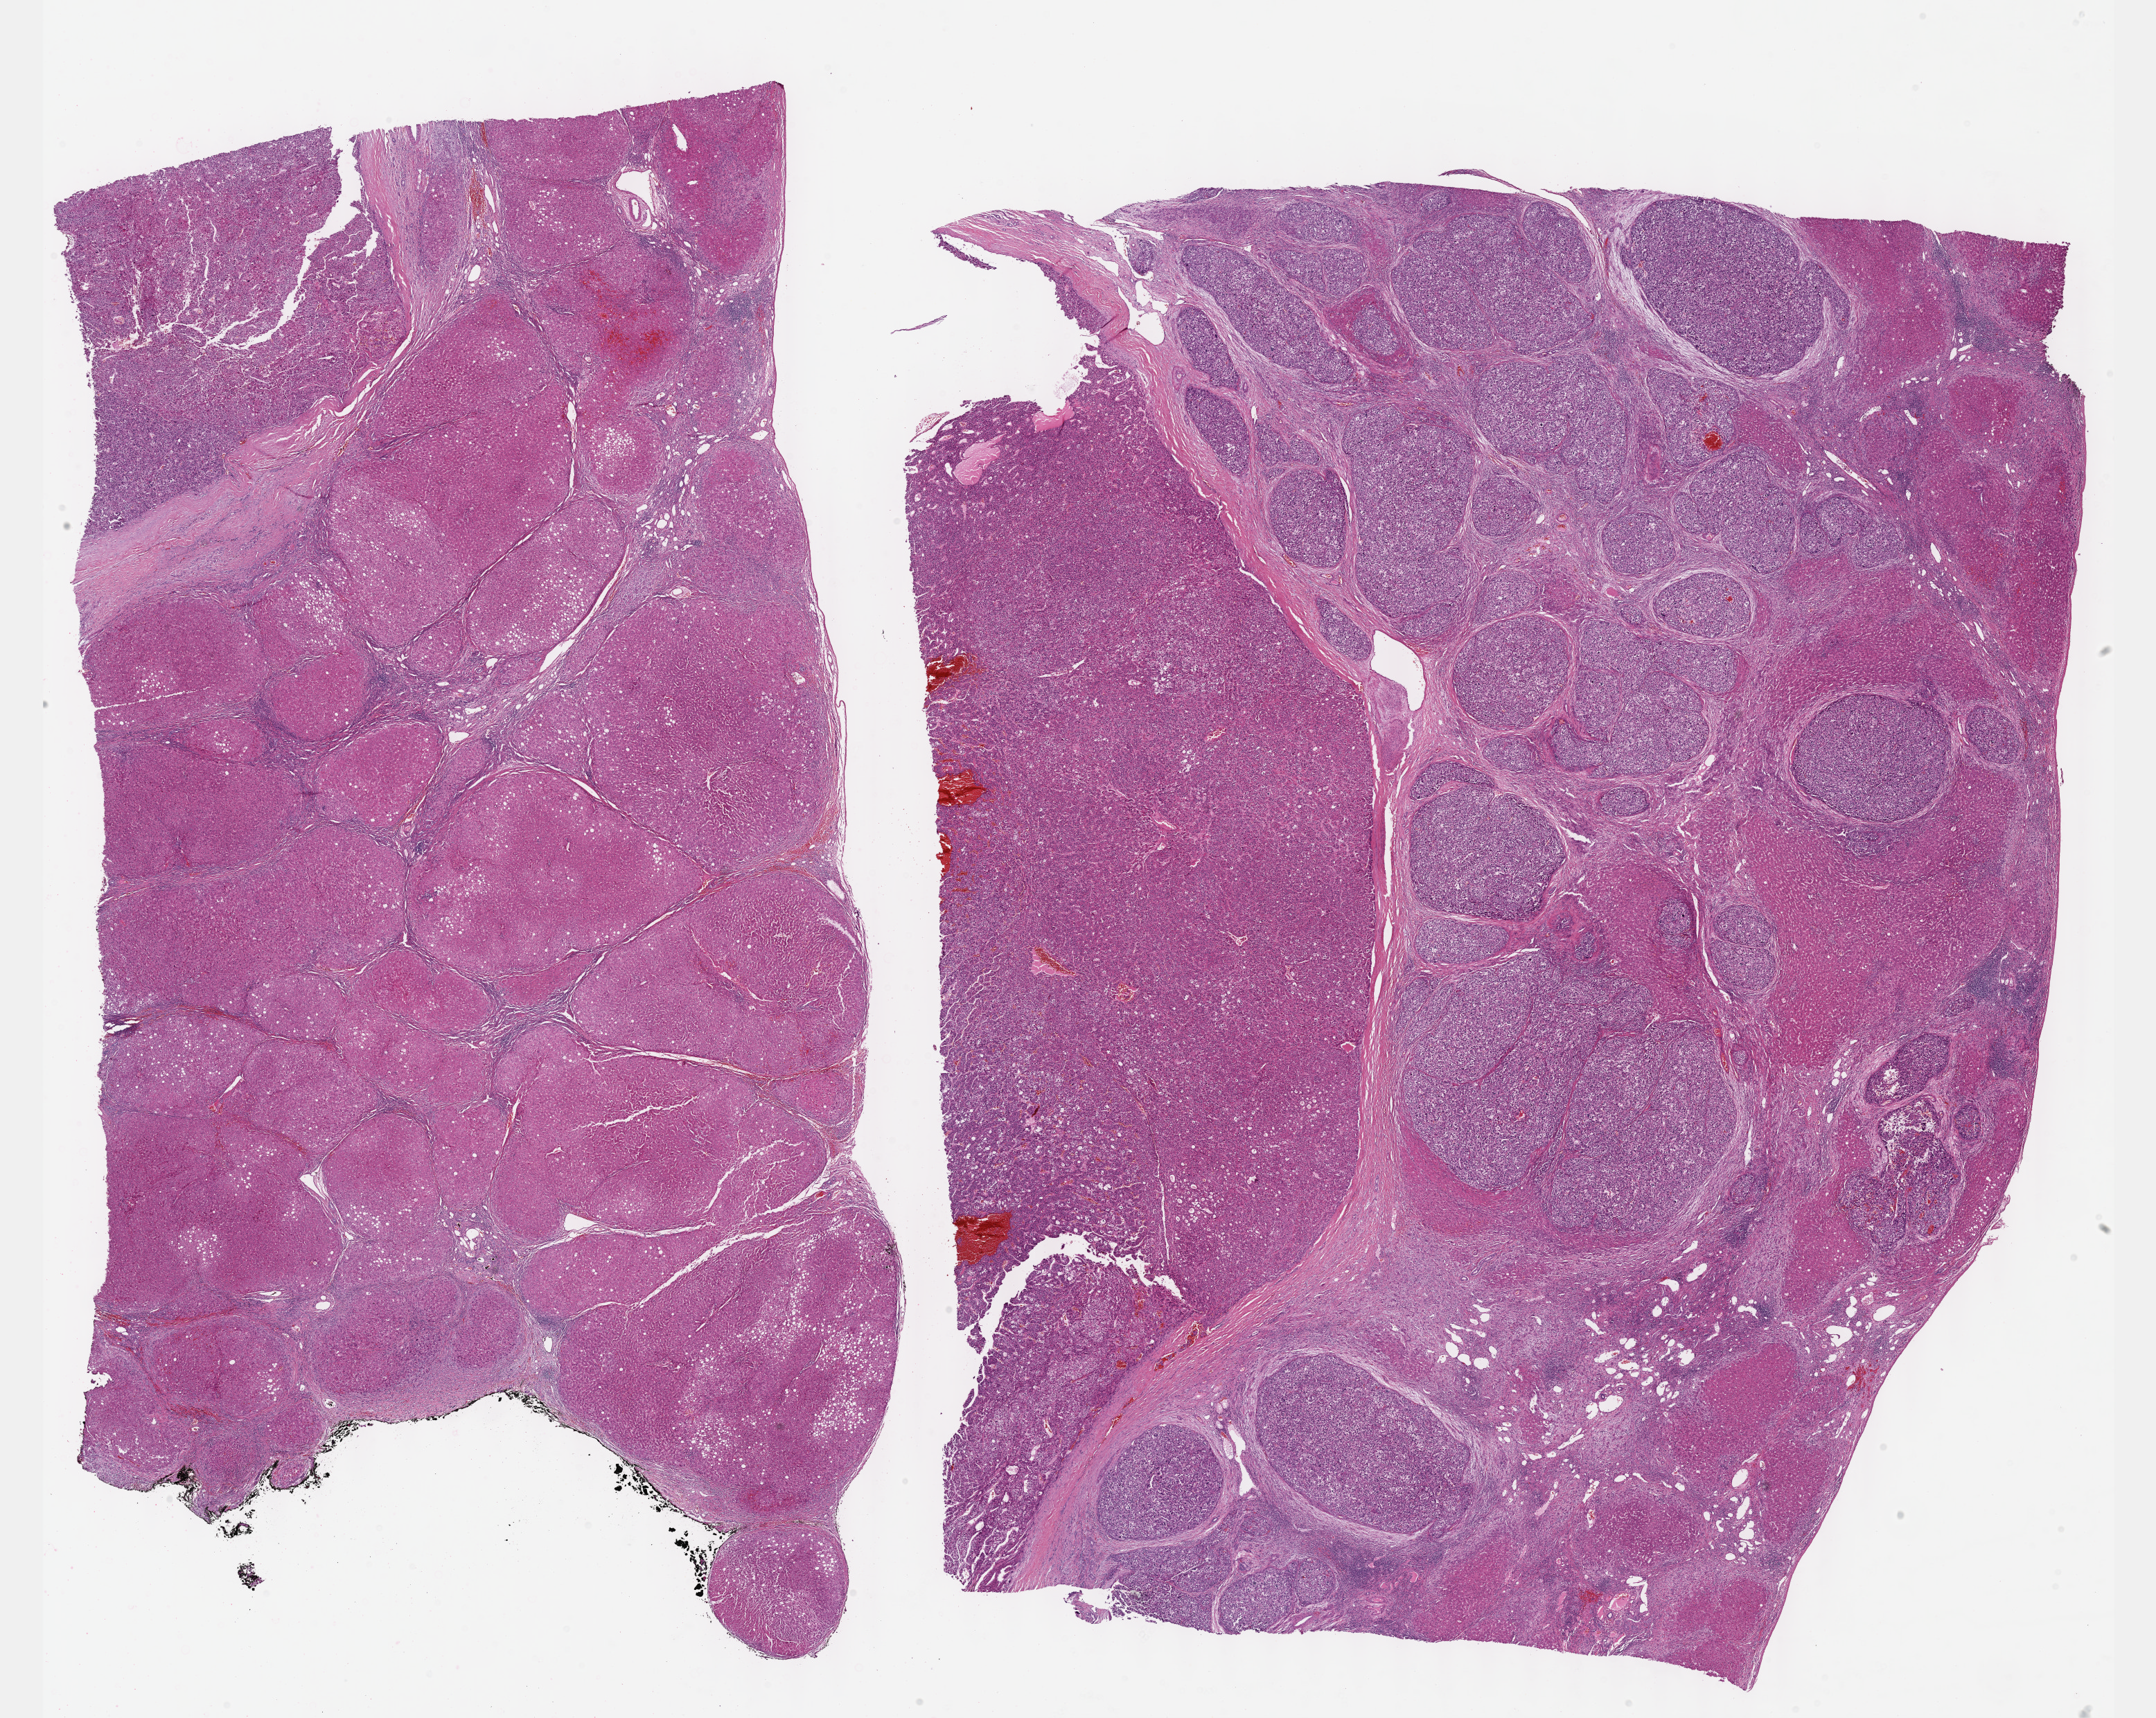
Hematoxylin and eosin (H&E) stained whole-slide image — shown as a low-resolution overview of the whole scanned area (about 25.1 x 20.0 mm). Formalin-fixed paraffin-embedded (FFPE) diagnostic section. Primary tumour sample from the liver. Patient: male, age at initial diagnosis 66 years. Histologic grade: G2 (moderately differentiated).
Pathologic diagnosis: Hepatocellular carcinoma, NOS. TNM: T2 NX MX. AJCC pathologic stage: II (7th edition).